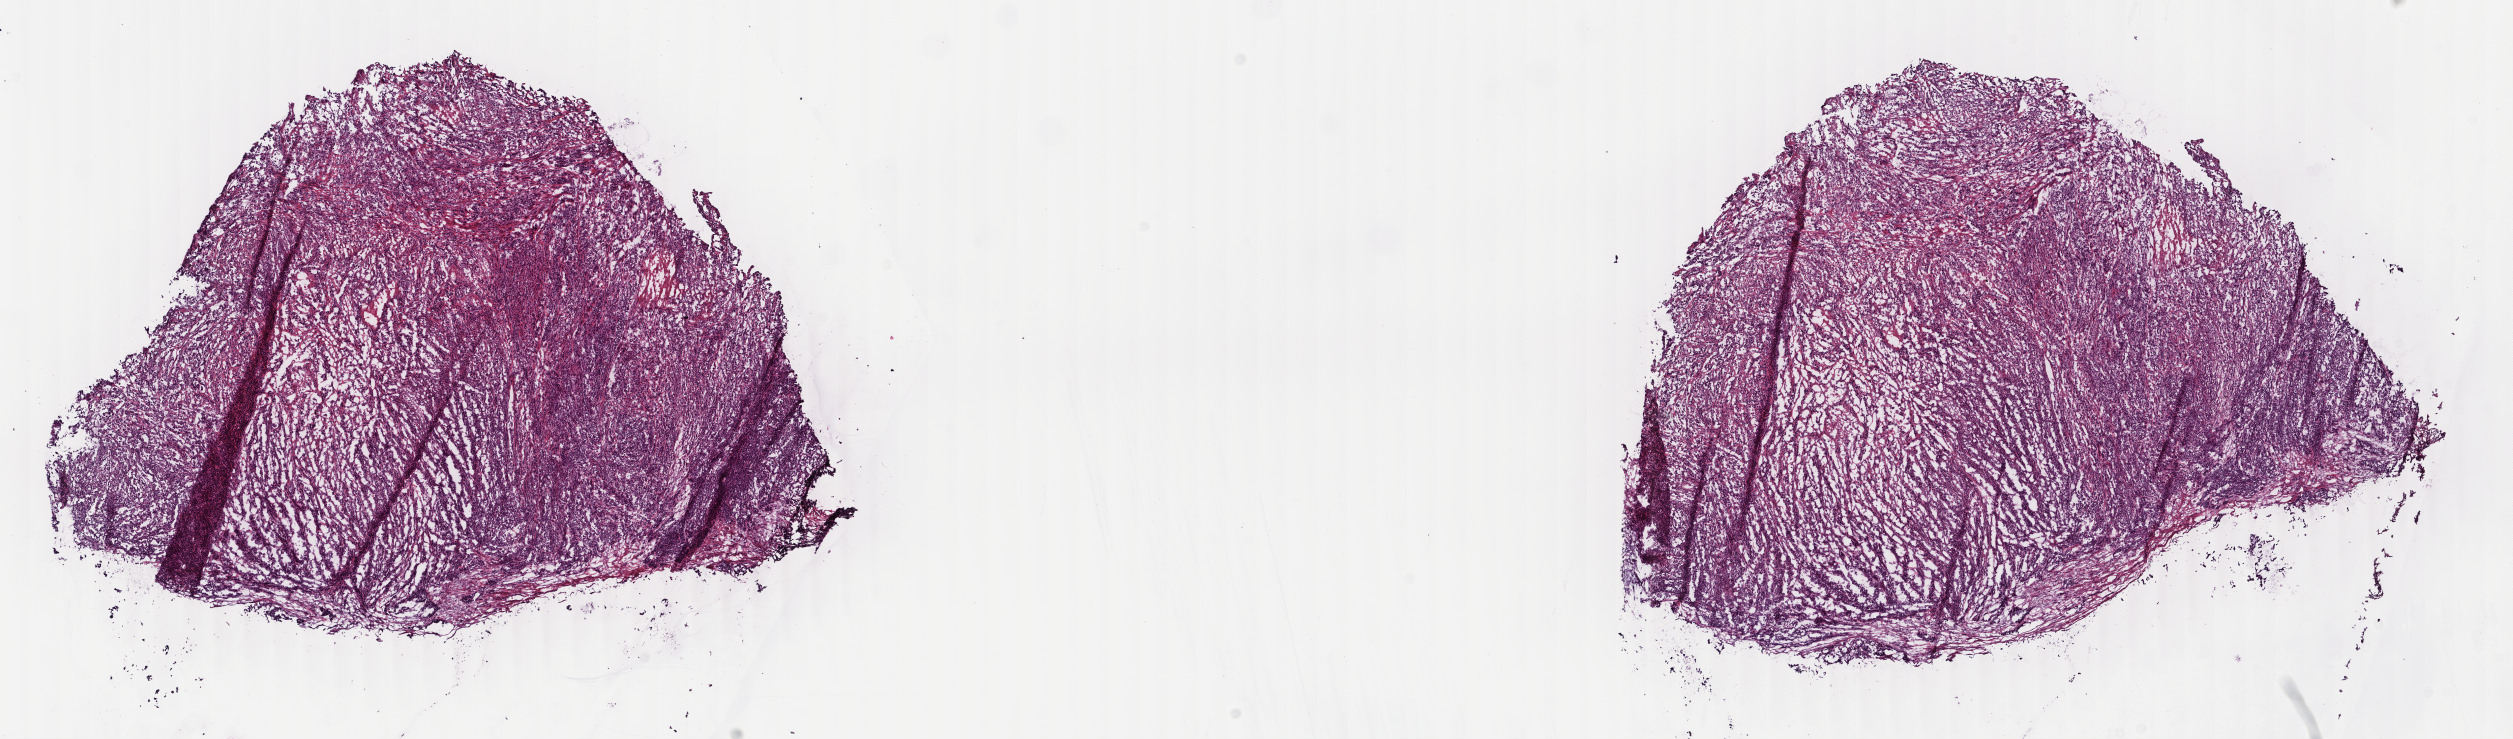
Whole-slide histology image, Hematoxylin and eosin (H&E) stained, a low-resolution overview of the entire scanned area, about 20.0 x 5.9 mm (from a 40x scan), frozen section from the bottom of the tissue portion, uterus, primary tumour sample. Patient: female, age at initial diagnosis 75 years. Histologic grade: G3 (poorly differentiated). Composition of this section per pathologist review: tumour cells 80%, tumour nuclei 90%, normal cells 10%, stromal cells 5%, necrosis 5%. Inflammatory infiltration, as recorded: lymphocyte infiltration 1%, monocyte infiltration 0%, neutrophil infiltration 0%.
FIGO stage: IB. Pathologic diagnosis: Serous cystadenocarcinoma, NOS (endometrium).